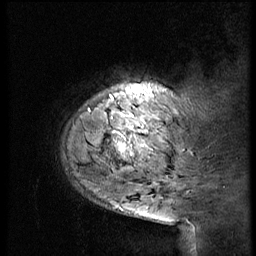
Breast MRI (dynamic contrast-enhanced), one sagittal slice; slice 9 of 56 in the series (ordered by position); 3 images stored at this slice position (order not interpretable as contrast timing); 1.5 T; TE 4.2 ms, TR 9 ms; 2.5 mm slice thickness; 256 × 256 image matrix. Patient: female, 51 years. From the clinical record (not read from this slice): setting: breast cancer imaged before/during neoadjuvant chemotherapy; receptor status: triple-negative.
Outlined on this slice (semi-automatic segmentation, software-assisted and operator-edited):
- analysis volume of interest (the breast-tissue region the enhancement analysis was run in; not a lesion): bounding box (x1, y1, x2, y2) in pixels: (56, 68, 183, 179)
- tumour enhancement mask (voxels above the 140 % enhancement threshold inside the analysis volume of interest): (110, 92, 145, 157)